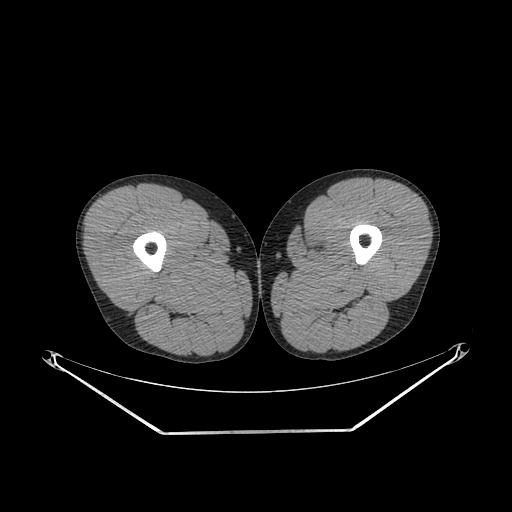
CT of an extremity soft-tissue mass (from a PET/CT study), one axial slice; position 263 of 311 along the scan axis; reconstruction kernel SOFT; soft-tissue window (W 400 / L 40 HU); 3.75 mm slice thickness; 512 × 512 image matrix, field of view 500 × 500 mm. Male patient. Case-level facts recorded for this patient, not image findings: histological type: mixoid liposarcoma; grade: low; site of the primary tumour: left thigh.
Structures marked on this image (expert contour drawn on MRI and transferred to this co-registered scan by the dataset authors):
- gross tumour volume (mass): bounding box (x1, y1, x2, y2) in pixels: (304, 237, 321, 250)